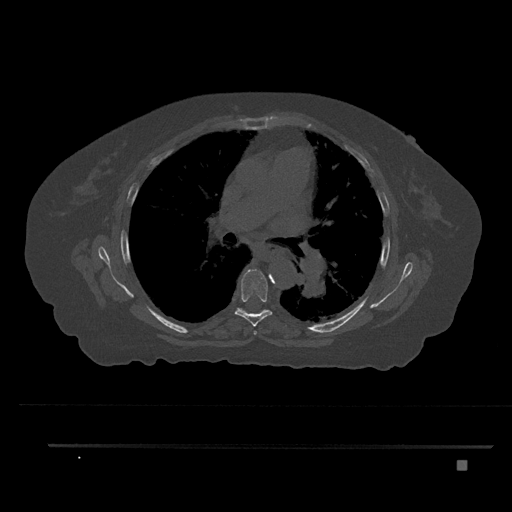
CT including the spine, one axial slice. Position 526 of 797 along the scan axis. Bone window (W 1800 / L 400 HU). 512 × 512 image matrix, field of view 437 × 437 mm. Female patient, age 76 years. From the clinical record (not read from this slice): primary cancer: lung.
Outlined on this slice (semi-automatically segmented with operator editing):
- T5 vertebra: bounding box (x1, y1, x2, y2) in pixels: (253, 331, 257, 335)
- T6 vertebra: (234, 269, 273, 326)
- T7 vertebra: (237, 308, 267, 311)